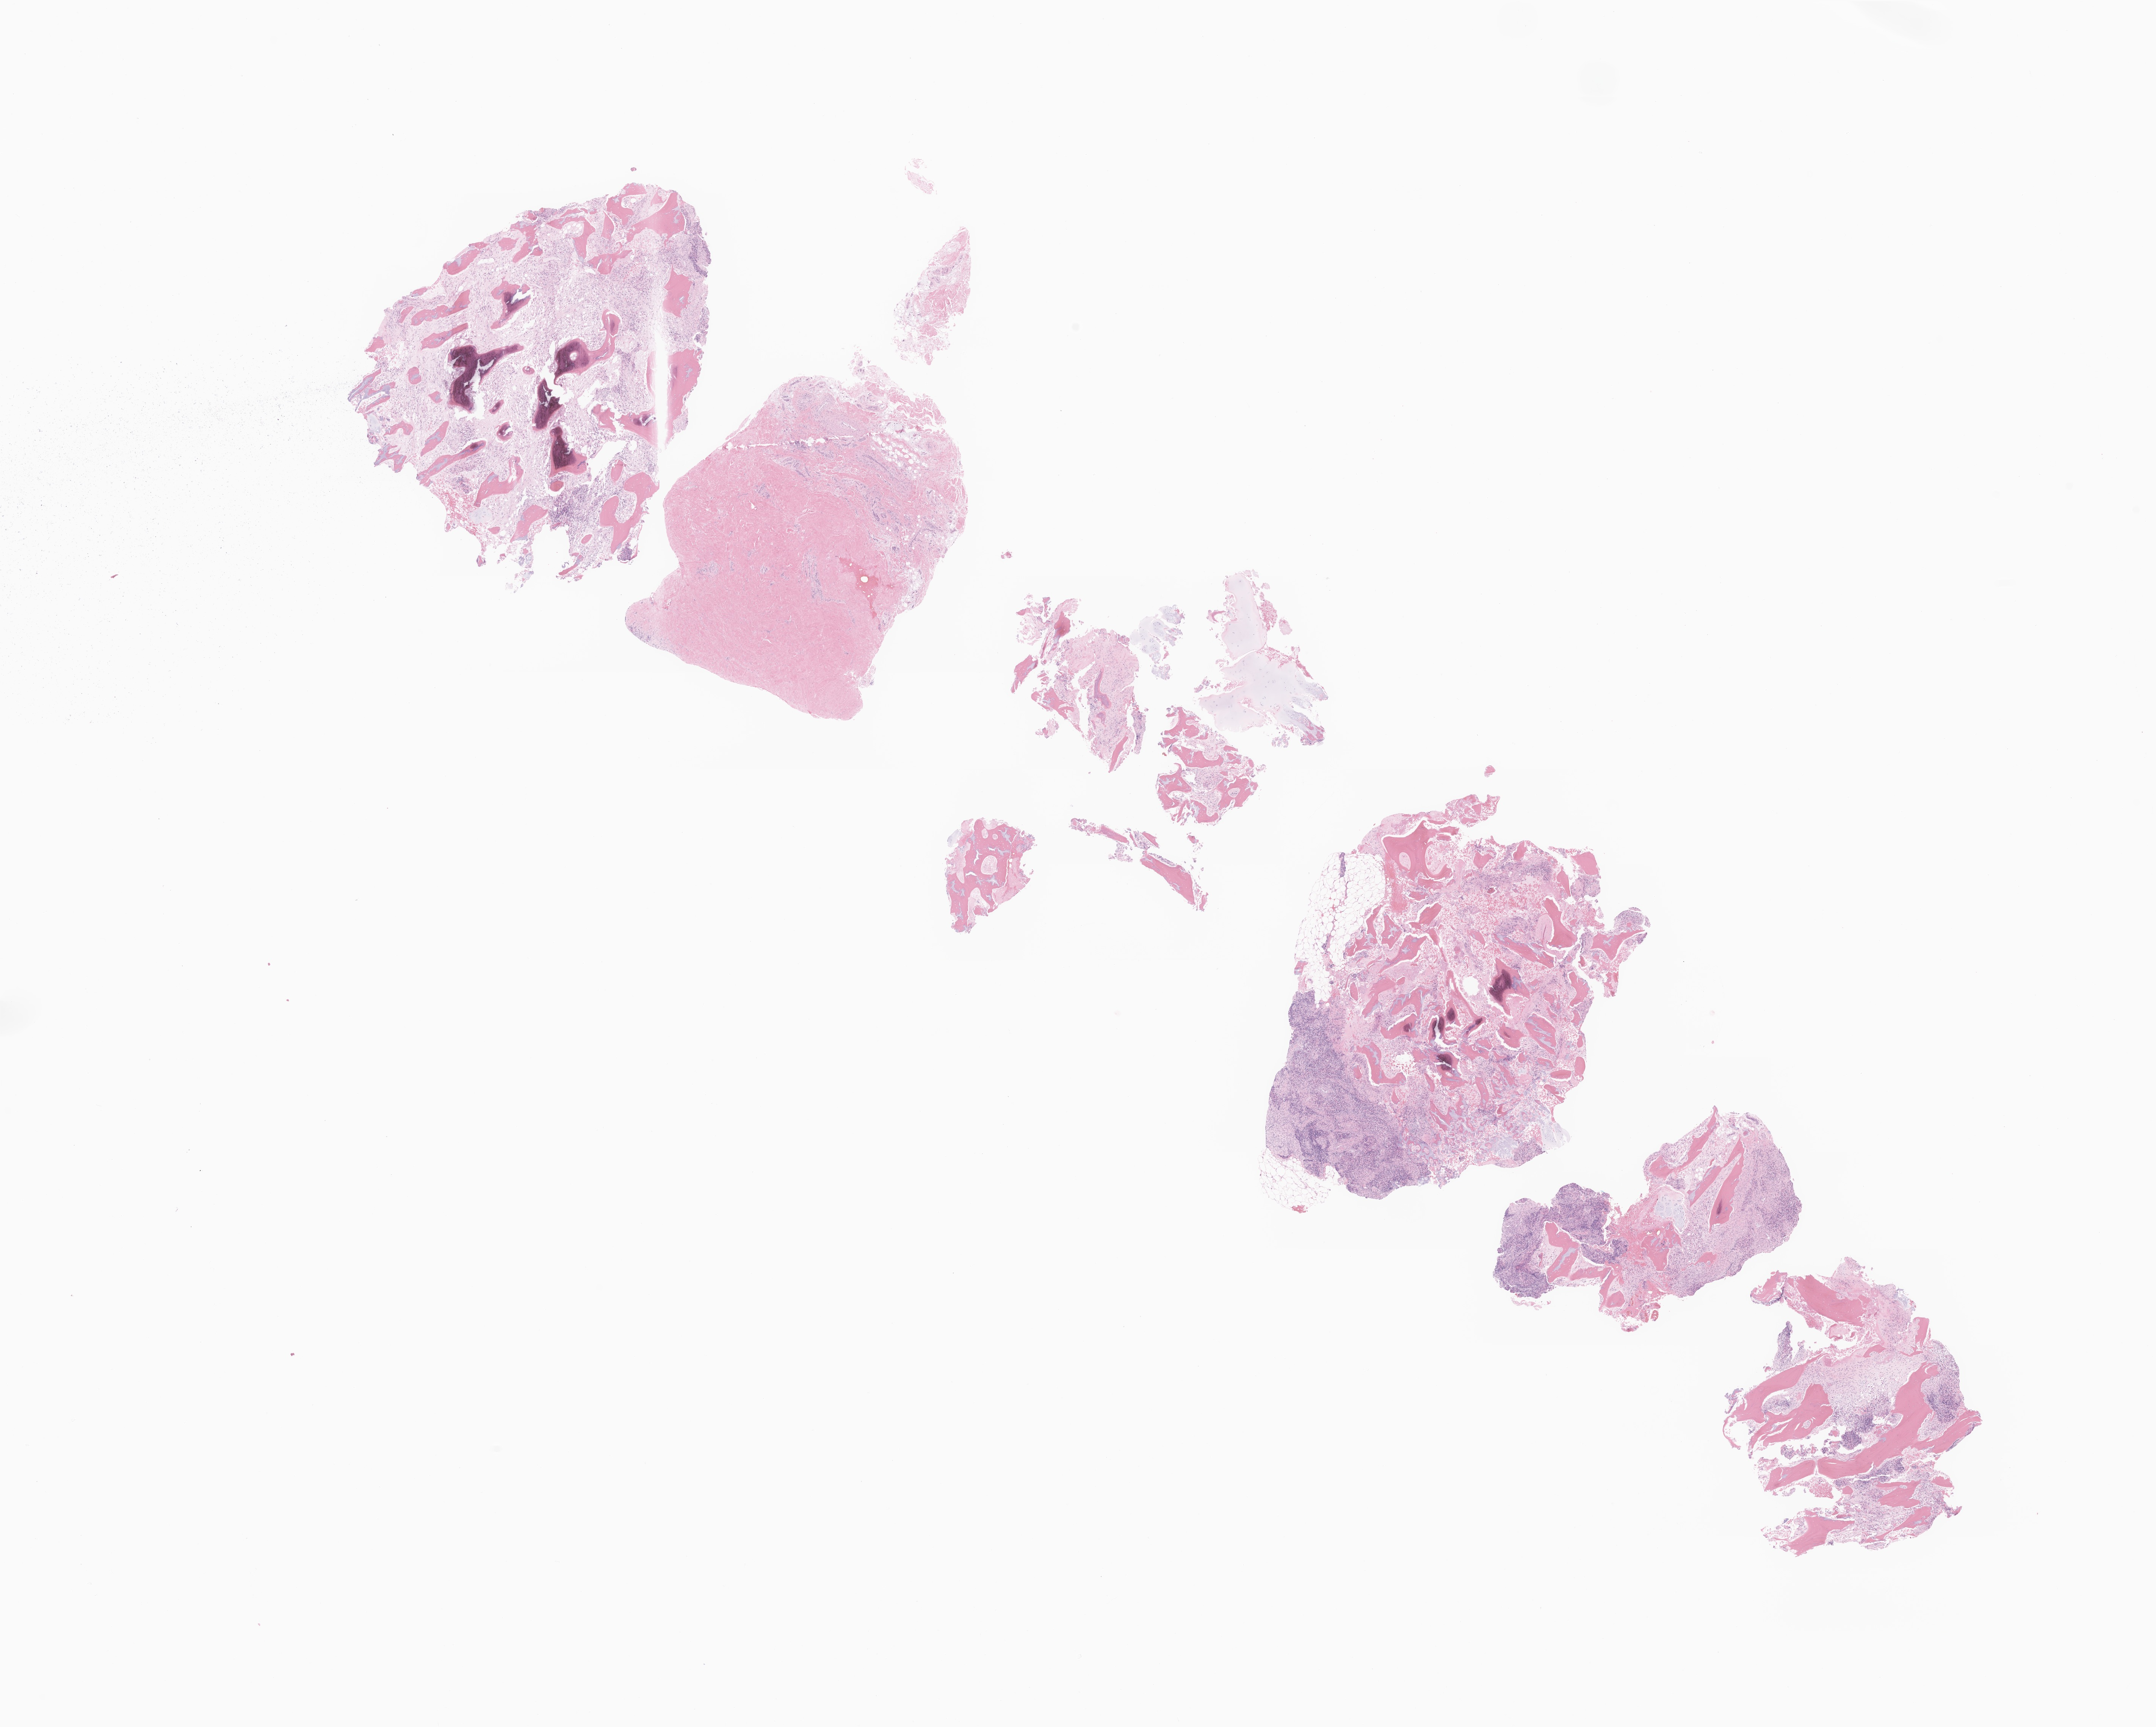
Whole-slide image, H&E stain of tumor tissue from the long bone of lower limb — whole scanned area (about 24.0 x 19.2 mm) shown as a low-resolution overview. FFPE section. Patient: male, age 56 months (4 years 8 months).
Diagnosis (ICD-O-3 morphology term): Alveolar rhabdomyosarcoma. Tissue or organ of origin (case record): long bones of lower limb and associated joints.